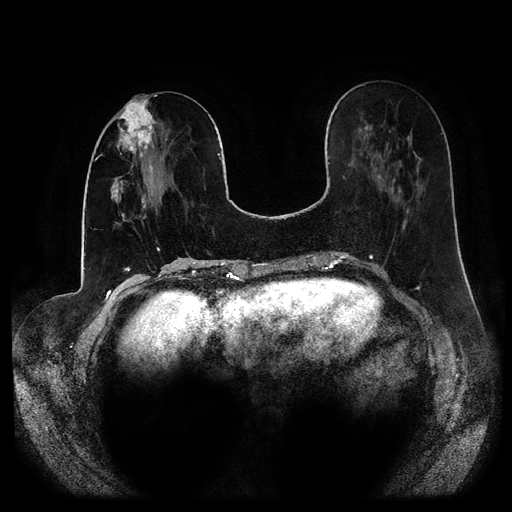
Breast MRI (dynamic contrast-enhanced, multi-phase), one axial slice. Slice 36 of 116 in the series (ordered by position). Dynamic contrast-enhanced series, time point 2 of 5 at this slice position (early post-contrast). 1.5 T. TE 2.6 ms, TR 5.2 ms. 2 mm slice thickness. 512 × 512 image matrix. Female patient, age 53 years.
Structures marked on this image (semi-automatic segmentation, software-assisted and operator-edited):
- breast lesion (labelled 'tumour' in the annotation; benign lesions carry a separate 'benign' label): bounding box [x1, y1, x2, y2] px = [115, 95, 160, 158]